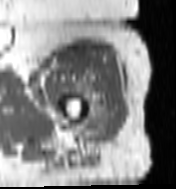
MRI of an extremity soft-tissue mass, one axial slice. Slice 89 of 100 in the series (ordered by position). MR volume resampled by the dataset authors to the PET/CT grid (not the native acquisition matrix). 176 × 189 image matrix, field of view 172 × 185 mm. Female patient. From the clinical record (not read from this slice): histological type: undifferentiated – high grade; grade: high; site of the primary tumour: left thigh.
Annotated regions visible in this slice (expert contour drawn on MRI and transferred to this co-registered scan by the dataset authors):
- gross tumour volume including surrounding oedema: bounding box <75,87,113,143> (left, top, right, bottom; pixels)
- gross tumour volume (mass): <85,116,106,131>